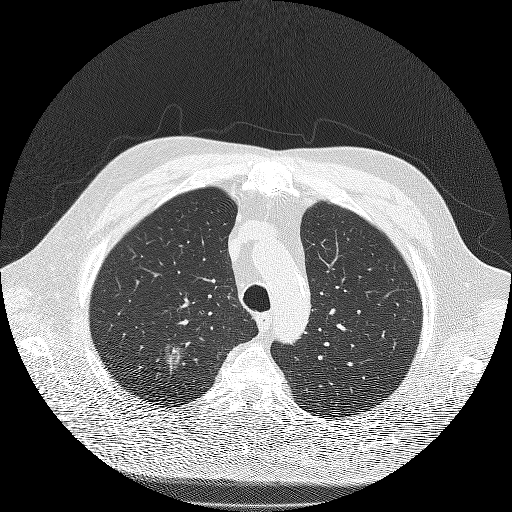
Chest CT (low-dose screening protocol), one axial image. Second annual screen. Lung window (W 1500 / L -600 HU). 2 mm slice thickness. 120 kVp. Slice 31 of 180 in the series. 512 × 512 image matrix, field of view 385 × 385 mm. Male participant, aged 71 years at enrolment.
Lesion marked by an expert reader, bounding box <140,328,202,390> (left, top, right, bottom; pixels). The screening reader recorded 3 non-calcified nodules or masses ≥4 mm on this exam (right upper lobe, right upper lobe, right lower lobe); which of them this box marks is not recorded.